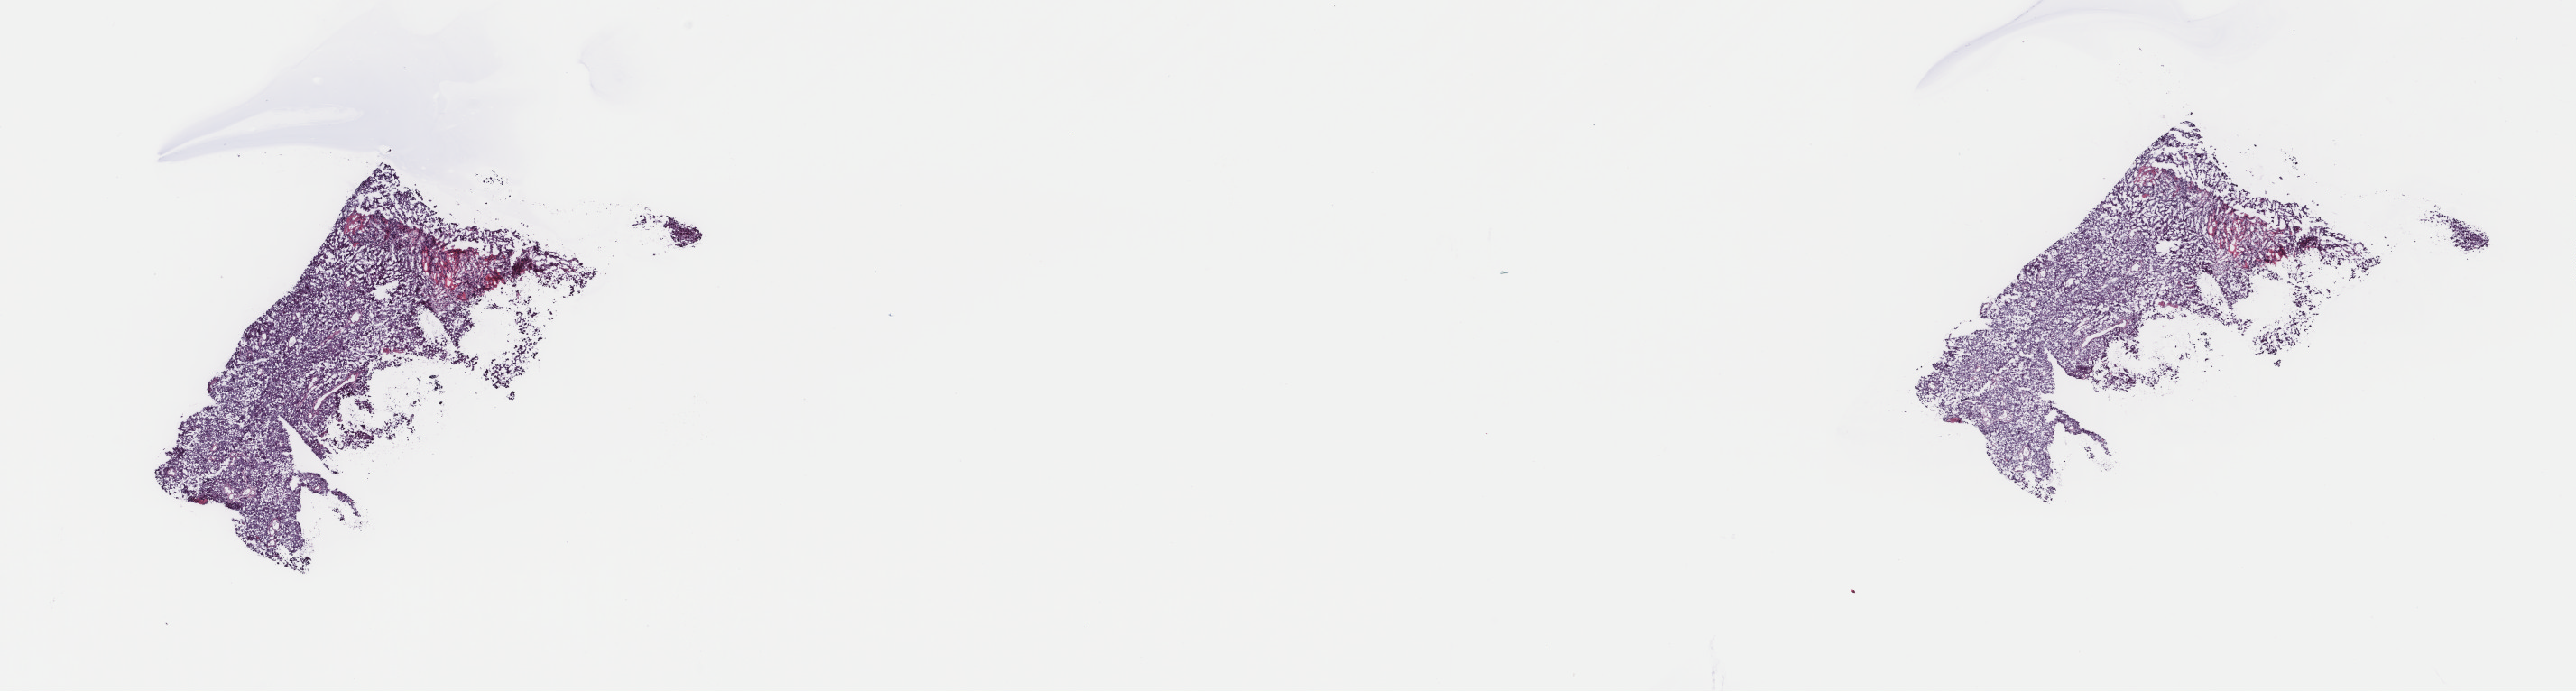
Digitized Hematoxylin and eosin (H&E) stained tissue section (whole slide) — a low-resolution overview of the entire scanned area, about 22.7 x 6.1 mm (from a 40x scan), frozen section from the top of the tissue portion, metastatic tumour sample, sampled site not recorded. Male, age 75 years at initial diagnosis. Composition of this section per pathologist review: tumour cells 100%, tumour nuclei 90%, normal cells 0%, stromal cells 0%, necrosis 0%. Infiltration values recorded for this section: lymphocyte infiltration 4%, monocyte infiltration 1%, neutrophil infiltration 0%.
This section: metastatic tumour tissue. Patient diagnosis: Malignant melanoma, NOS.